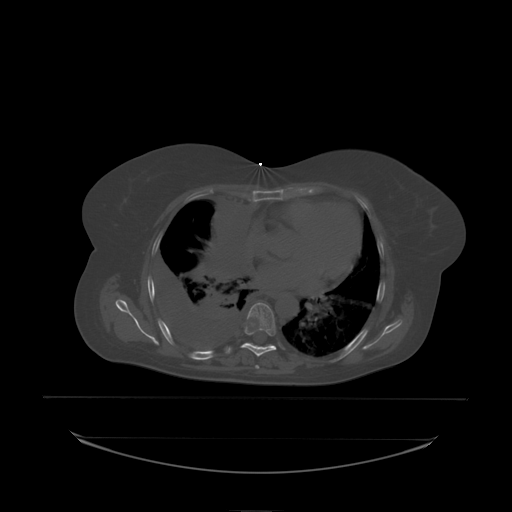
CT including the spine, one axial slice. Slice 141 of 242 in the series (ordered by position). Bone window (W 1800 / L 400 HU). 2.5 mm slice thickness. 512 × 512 image matrix, field of view 500 × 500 mm. Patient: female, 53 years. Case-level facts recorded for this patient, not image findings: primary cancer: lung.
Outlined on this slice (semi-automatically segmented with operator editing):
- T7 vertebra: bounding box (x1, y1, x2, y2) in pixels: (245, 303, 277, 336)